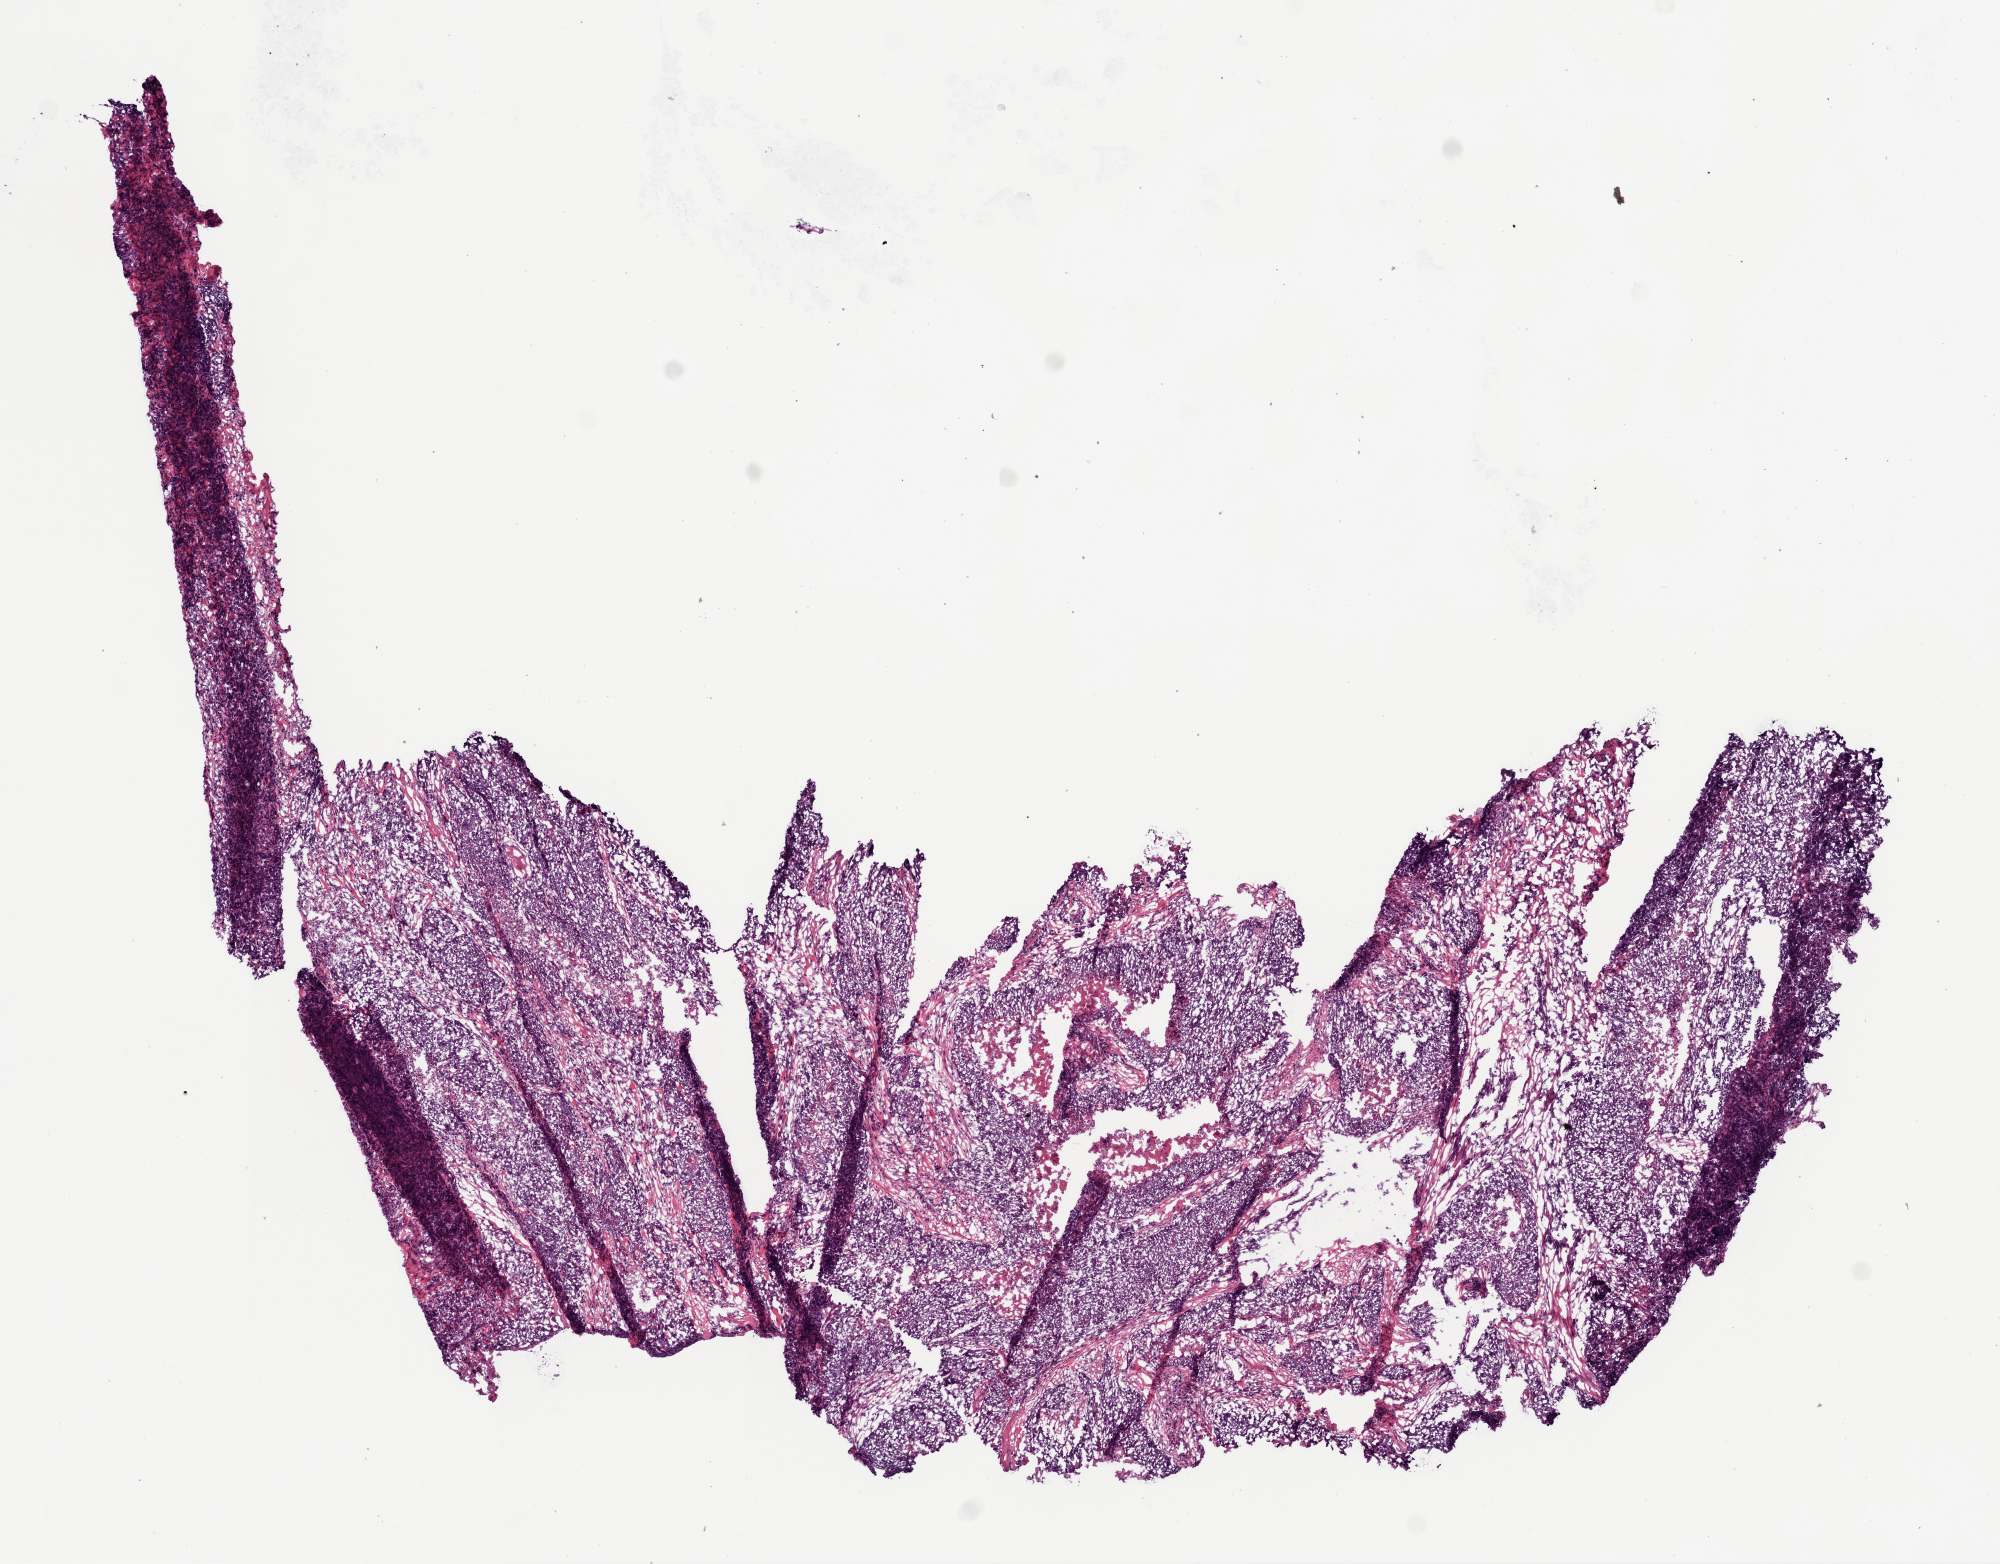
Hematoxylin and eosin (H&E) stained whole-slide image, low-resolution overview of the scanned area, about 8.0 x 6.3 mm; frozen section; head and neck, primary tumour sample. Male, age 63 years at initial diagnosis. Histologic grade: G3 (poorly differentiated). Slide review estimates, as recorded: tumour cells 70%, tumour nuclei 85%, normal cells 0%, stromal cells 20%, necrosis 10%.
Histologic diagnosis: Squamous cell carcinoma, NOS (larynx, NOS). AJCC pathologic stage: III.